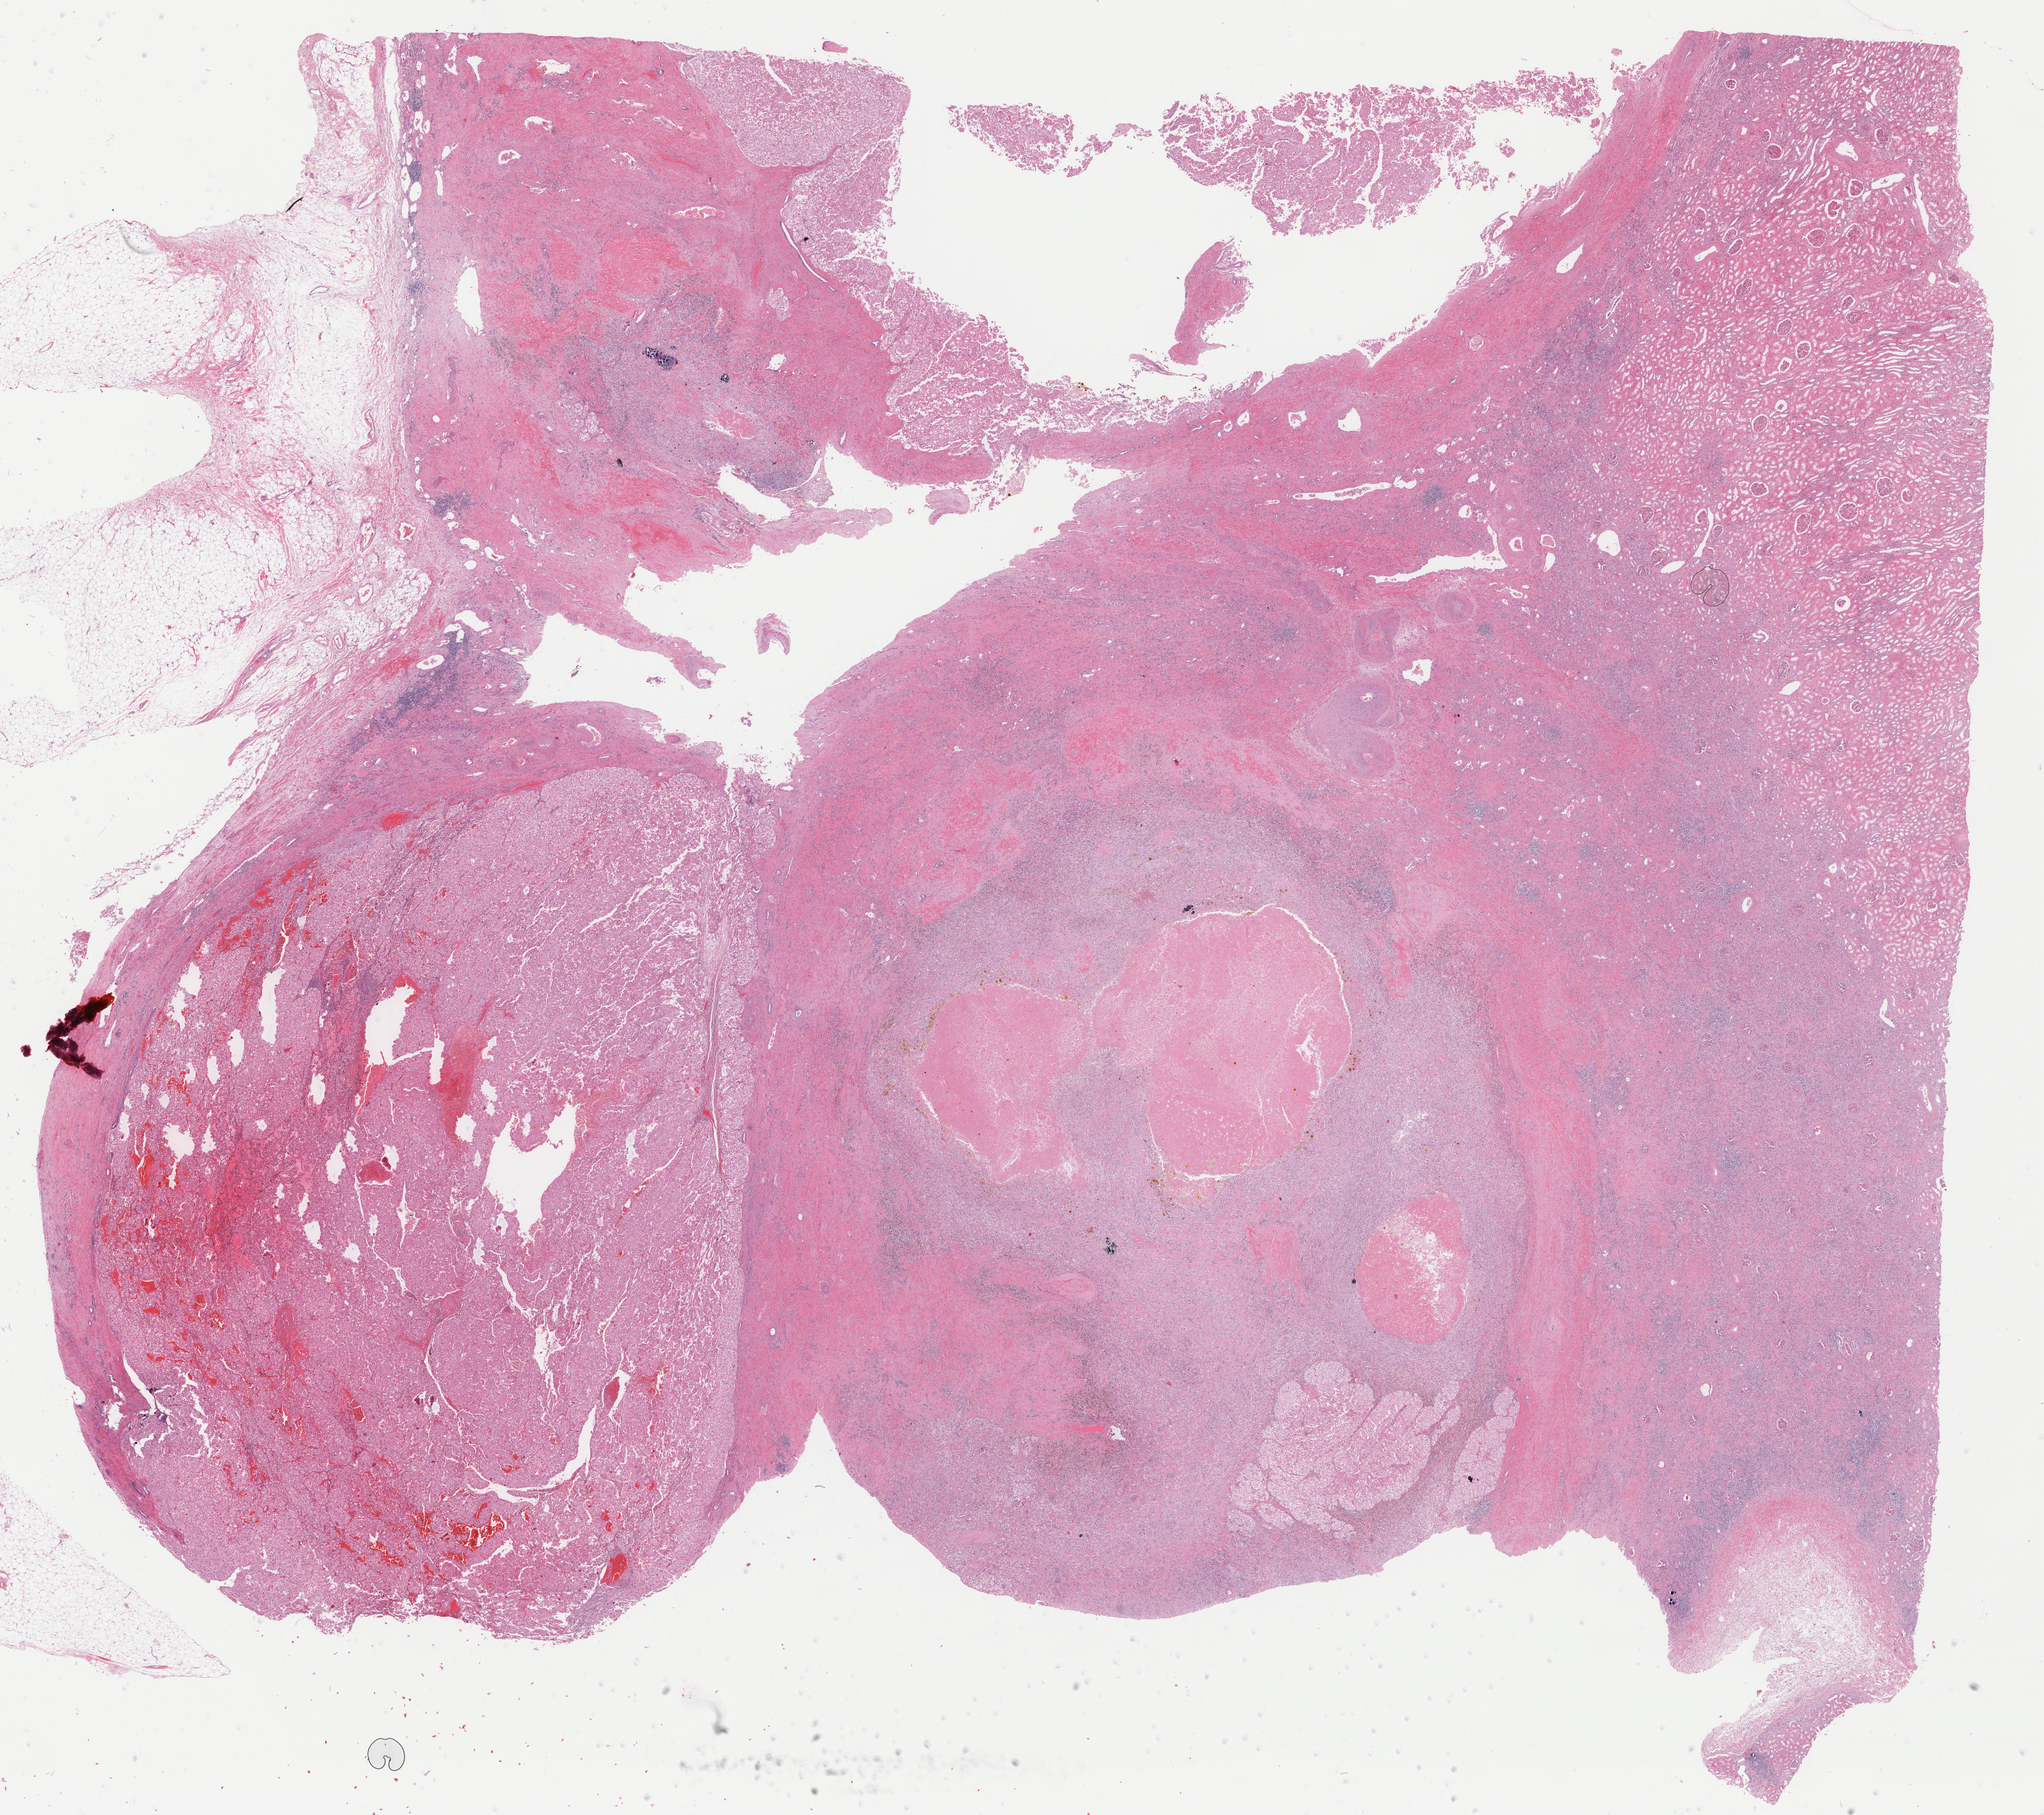
Hematoxylin and eosin (H&E) stained whole-slide image, shown as a low-resolution overview of the whole scanned area (about 24.2 x 21.5 mm, acquisition: 40x scan), formalin-fixed paraffin-embedded (FFPE) diagnostic section, primary tumour sample from the kidney. Patient: male, age at initial diagnosis 75 years.
AJCC pathologic stage: I. Histologic diagnosis: Renal cell carcinoma, chromophobe type.